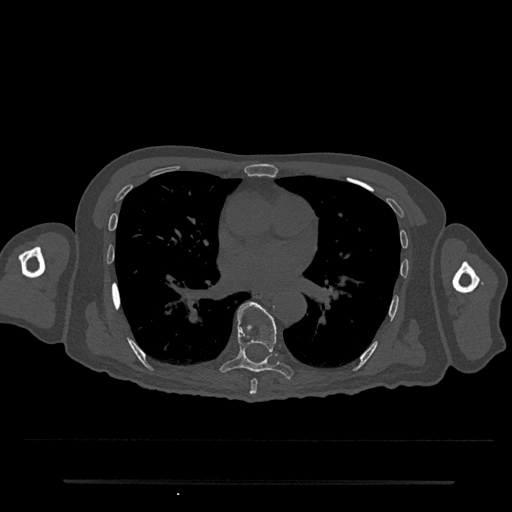
CT including the spine, one axial slice. Slice 431 of 797 in the series (ordered by position). 120 kVp. Bone window (W 1800 / L 400 HU). 0.5 mm slice thickness. 512 × 512 image matrix, field of view 427 × 427 mm. Male patient, age 74 years. From the clinical record (not read from this slice): primary cancer: prostate.
Outlined on this slice (semi-automatically segmented with operator editing):
- T7 vertebra: box from (x=250, y=379) to (x=258, y=395) px
- T8 vertebra: (x=219, y=302)–(x=294, y=379)